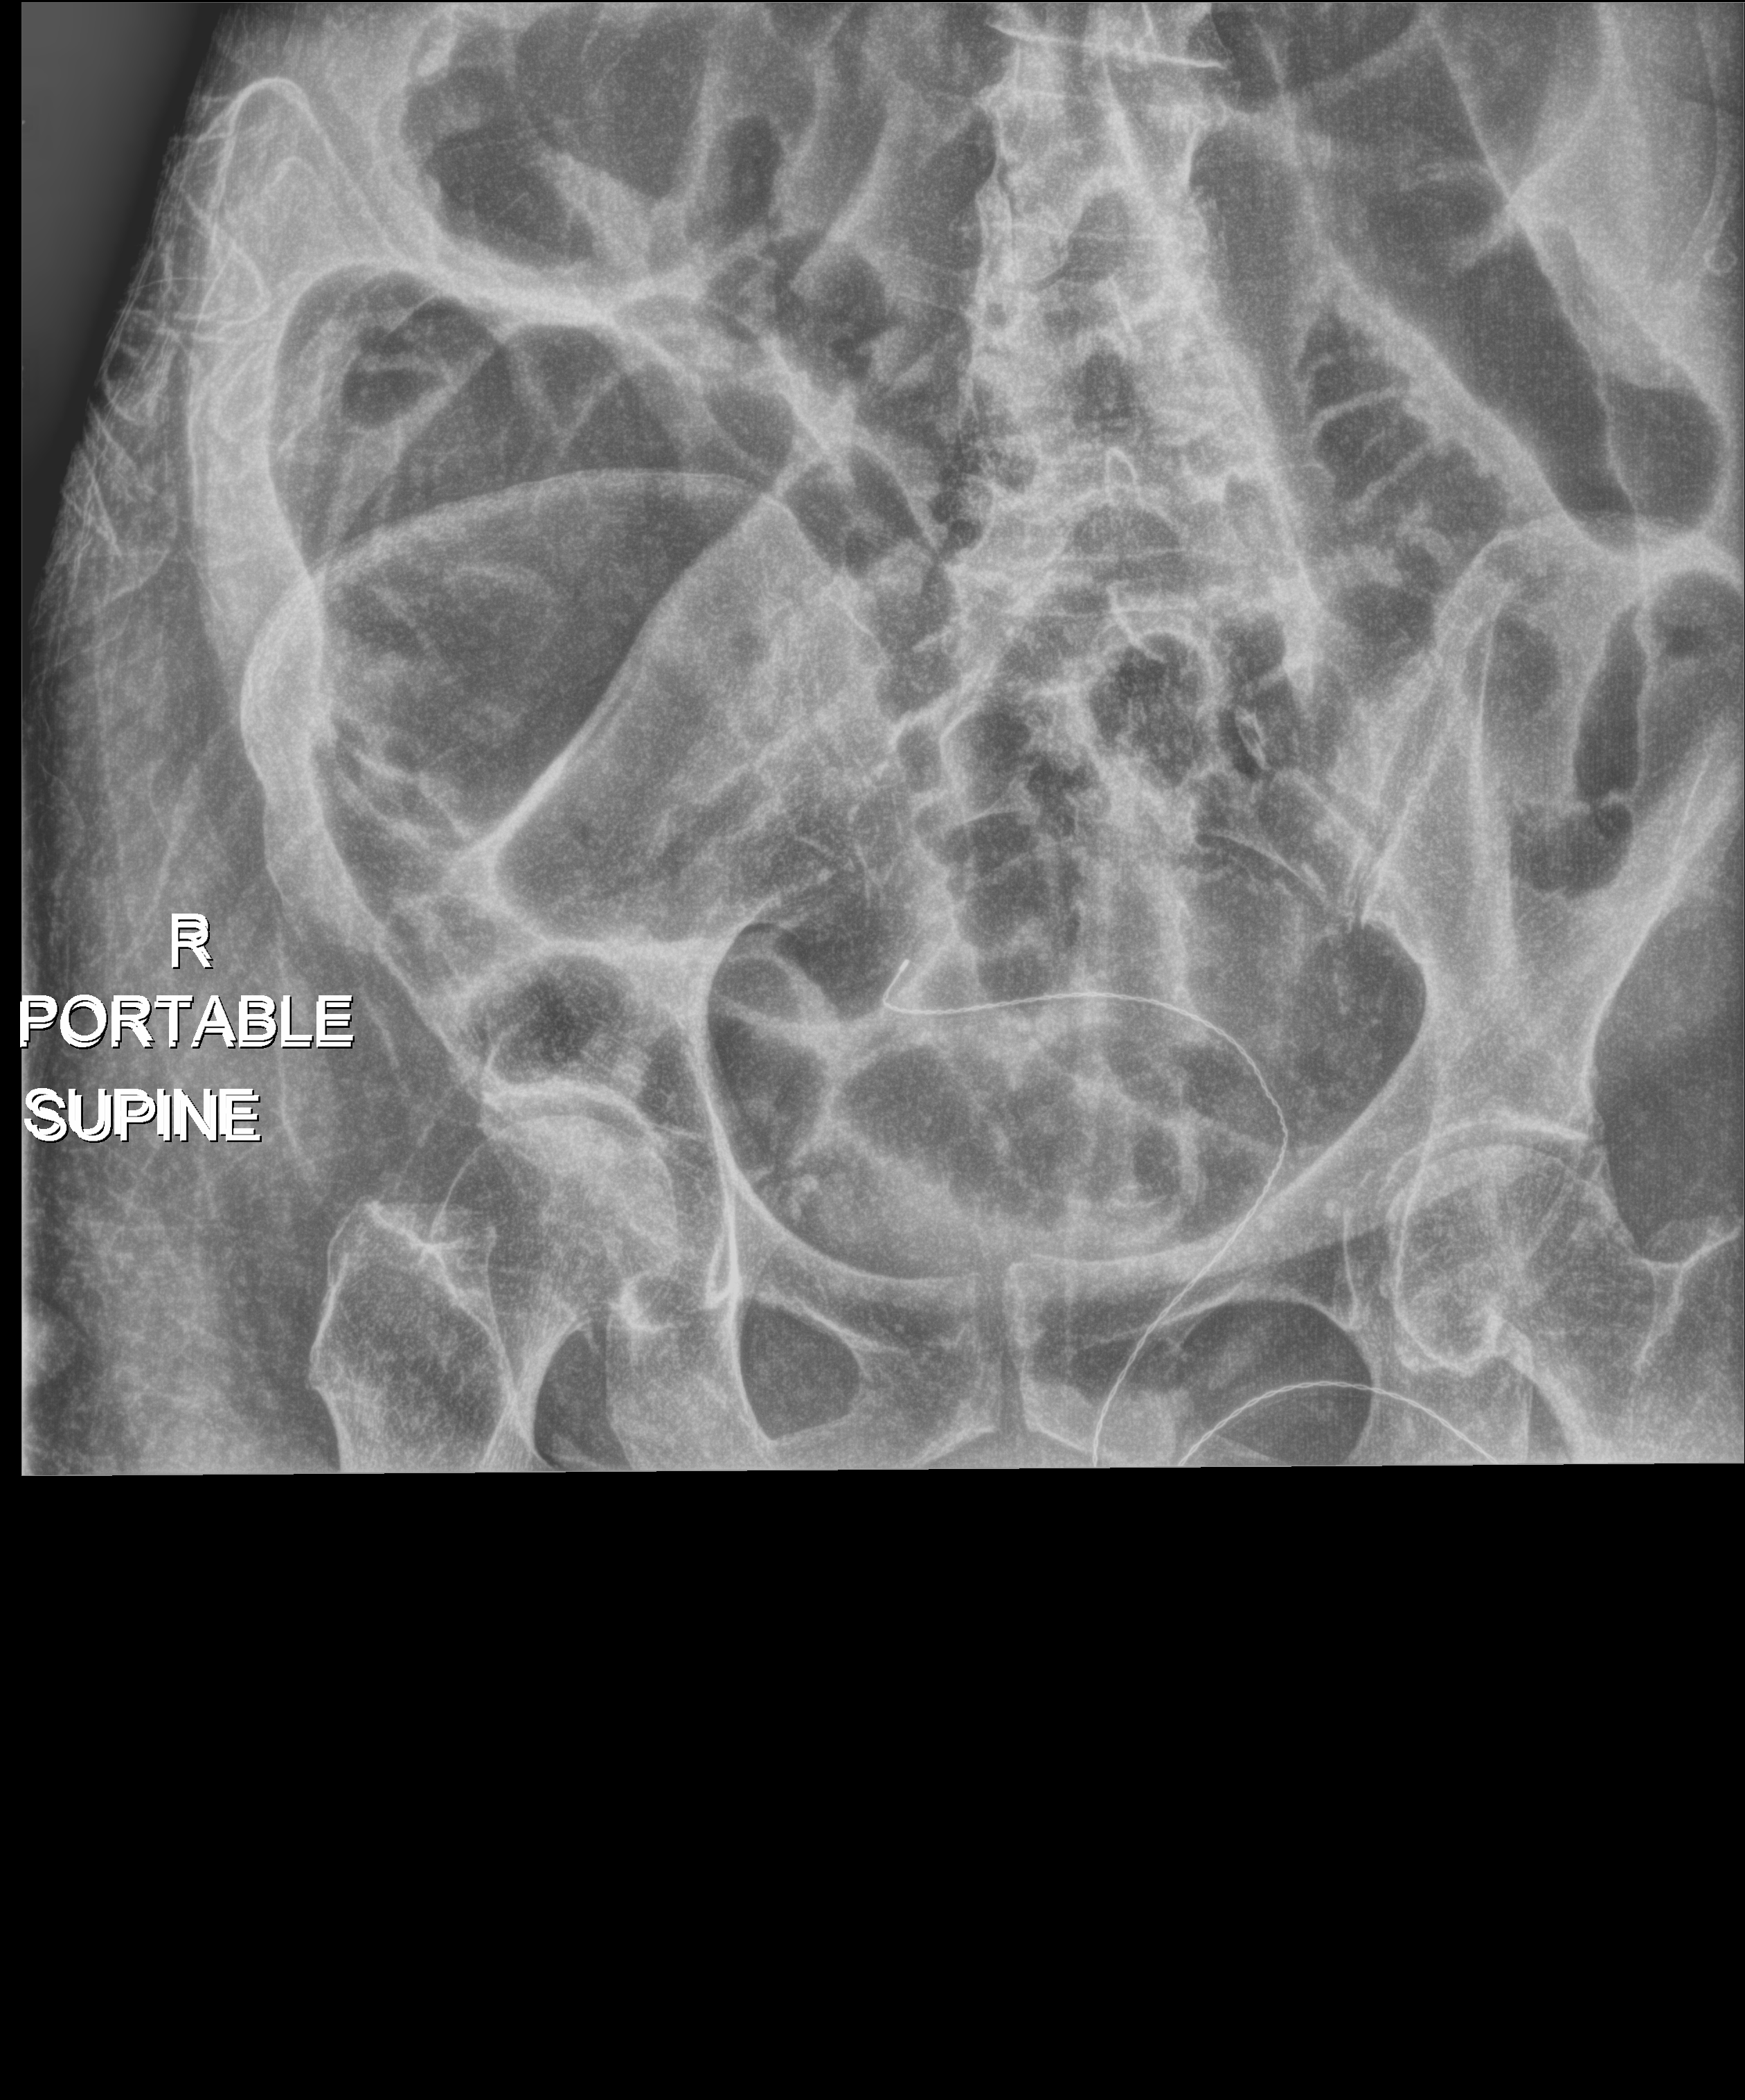
Bedside abdomen radiograph (digital radiography), anteroposterior (AP) projection. Female patient hospitalised with COVID-19, age 60–74 years.
From the hospital-stay record, not from the radiograph (when in the stay this image was taken is not recorded): mechanically ventilated during this hospital stay: yes.